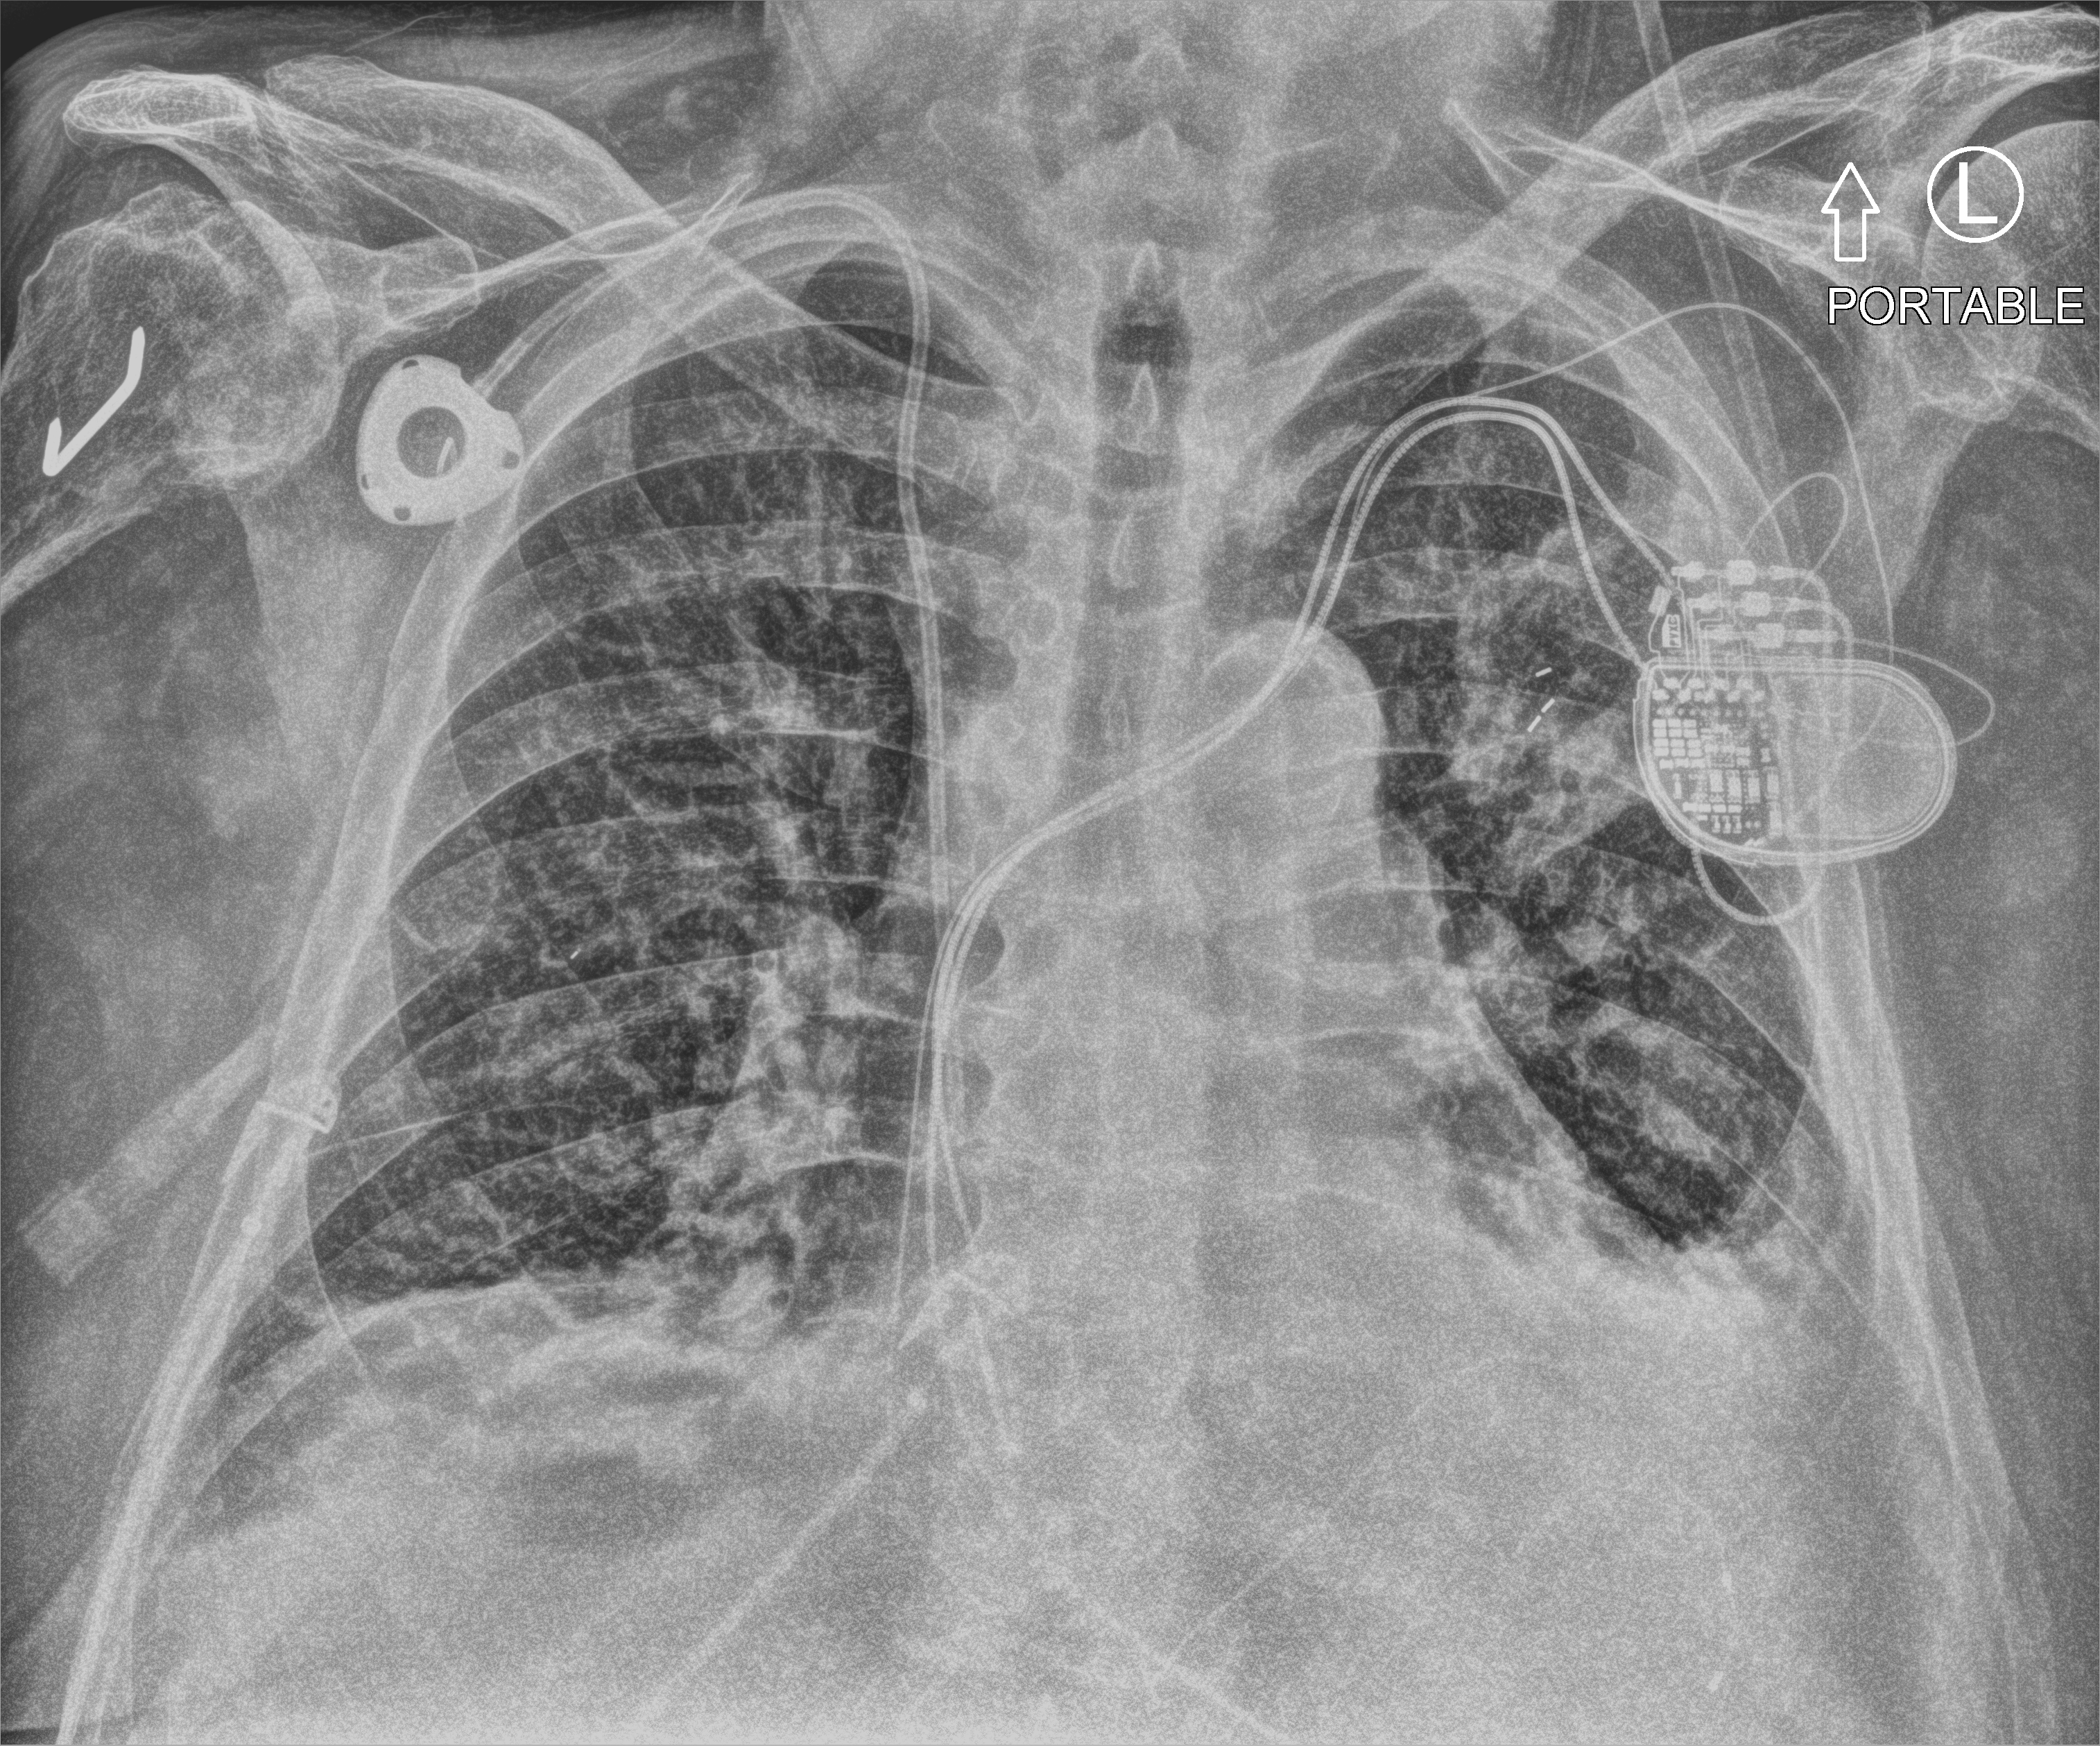
Chest X-ray (portable); anteroposterior (AP) projection. Male patient hospitalised with COVID-19, age 60–74 years.
Admission-level facts for this patient (not findings on this image; timing relative to this image not recorded):
- mechanically ventilated during this hospital stay: no
- admitted to intensive care during this hospital stay: yes
- length of hospital stay: 20 days